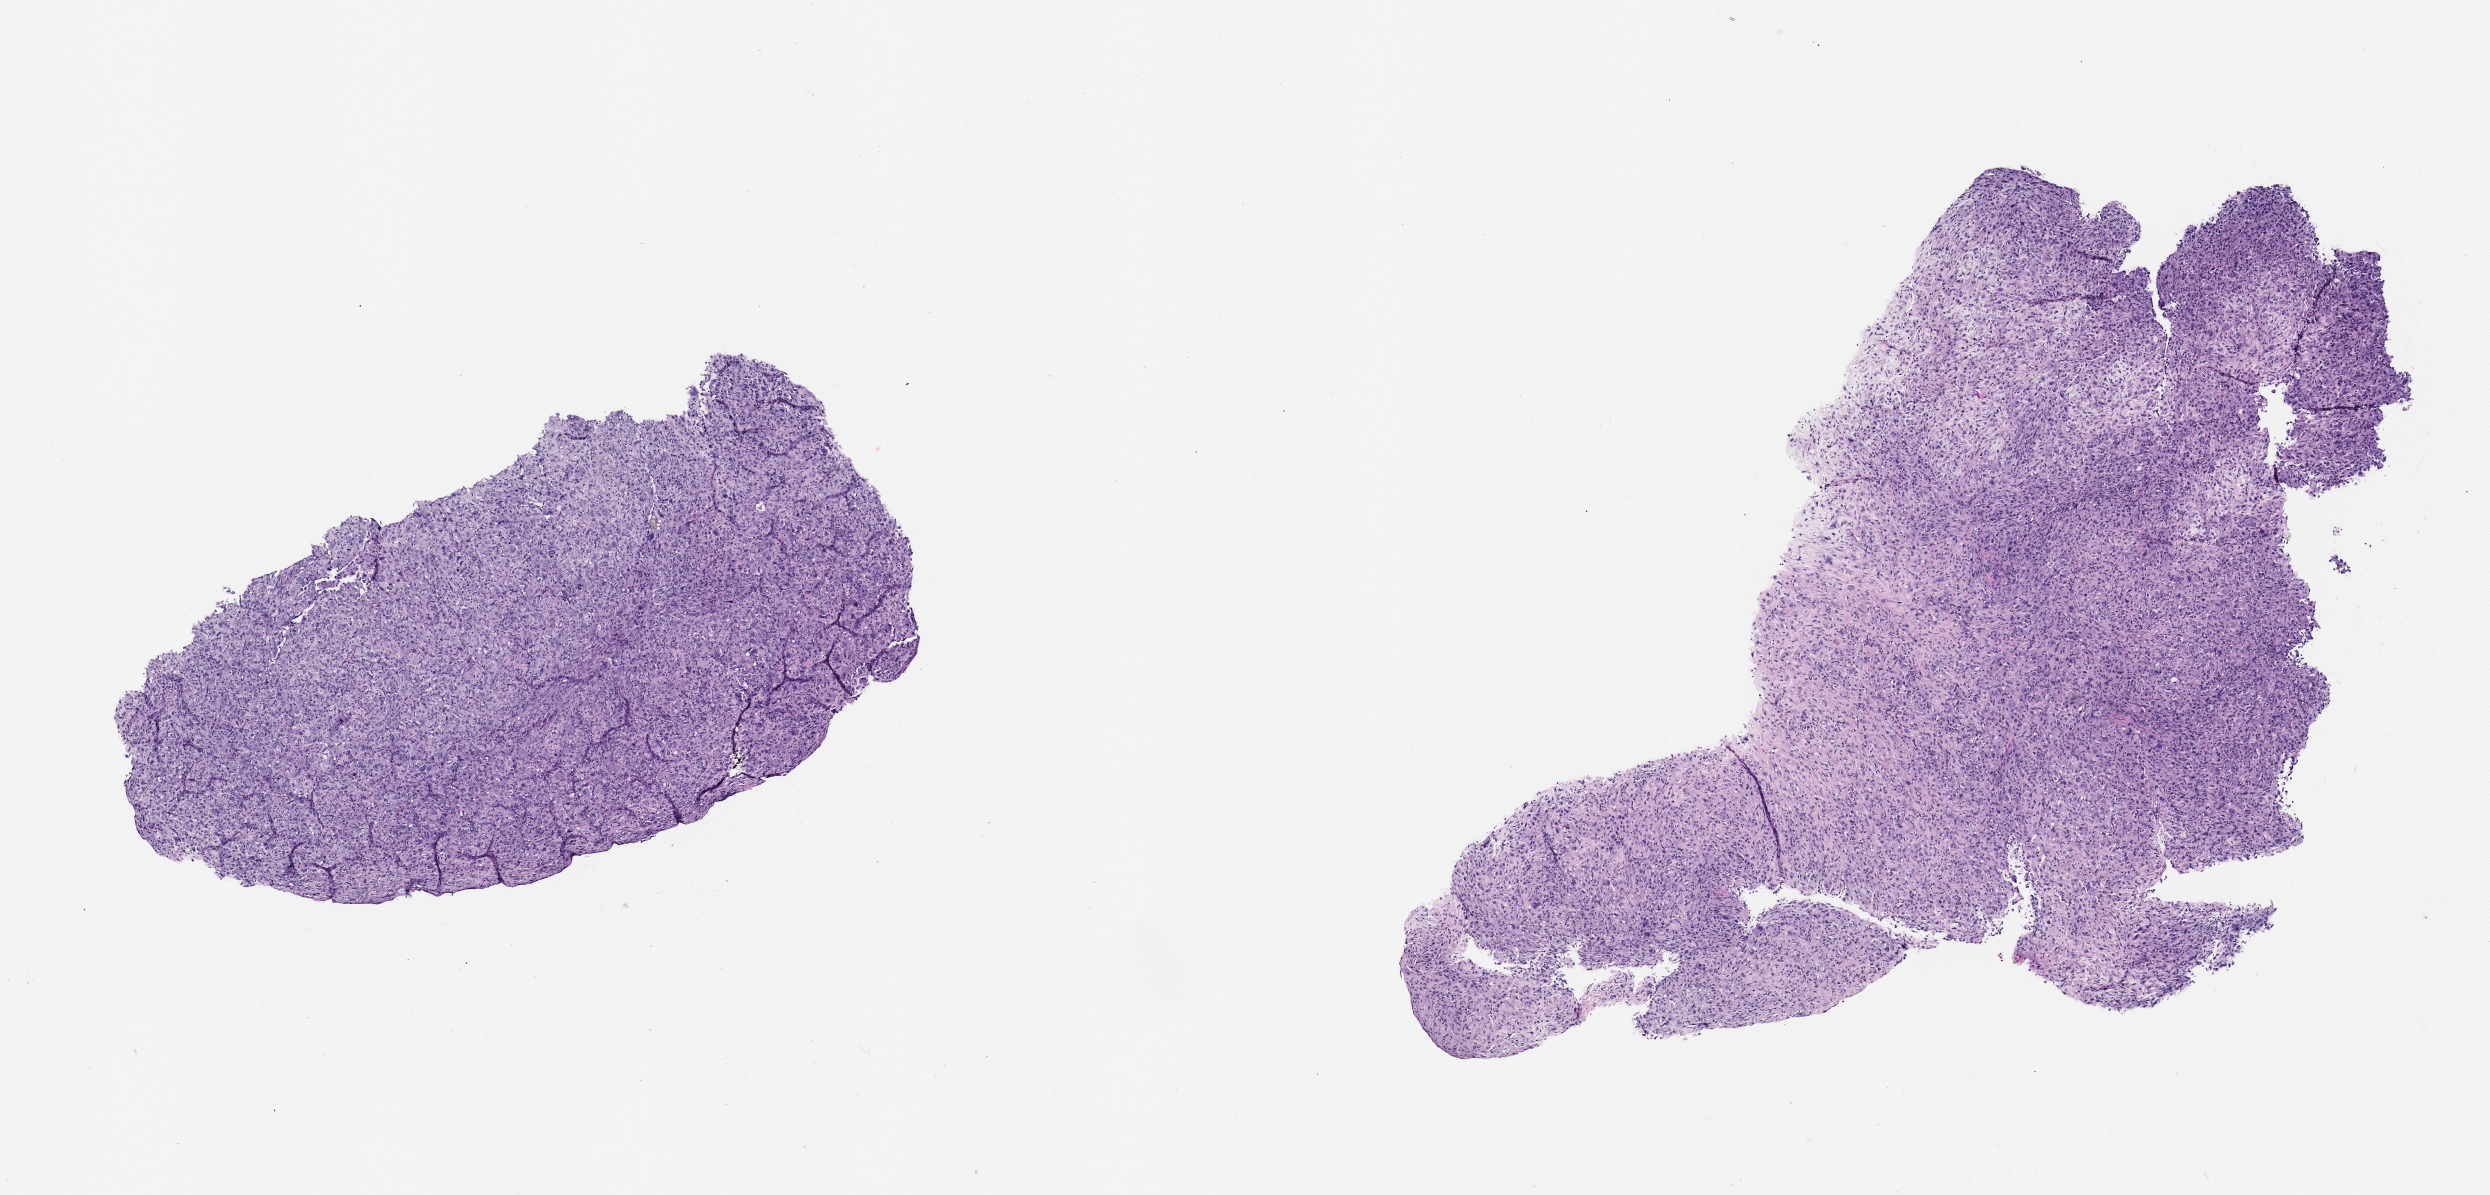
H&E whole-slide image of a patient-derived xenograft (PDX) tumor grown in a mouse, passage 2 — a low-resolution overview of the entire scanned area, about 10.0 x 4.8 mm; formalin-fixed, paraffin-embedded (FFPE) tissue; tumor site category: bone.
Originating patient diagnosis: Osteosarcoma.